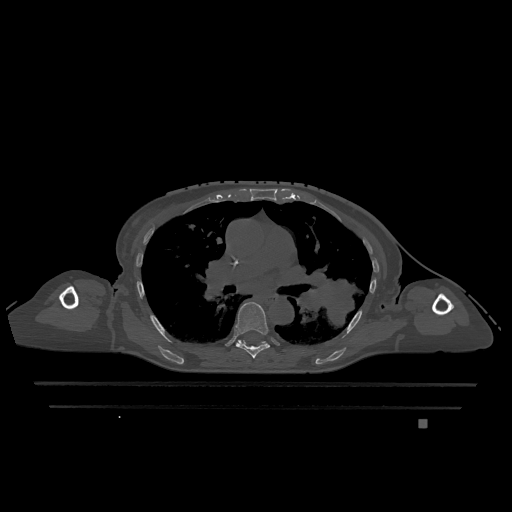
CT including the spine, one axial slice; position 780 of 1317 along the scan axis; bone window (W 1800 / L 400 HU); 512 × 512 image matrix. Patient: female, 74 years. From the clinical record (not read from this slice): primary cancer: lung; vertebrae with lytic lesions (as recorded): T1, T4, T5, T6, L4, L5.
Annotated regions visible in this slice (semi-automatically segmented with operator editing):
- T6 vertebra: box from (x=235, y=302) to (x=270, y=359) px
- T7 vertebra: (x=238, y=340)–(x=269, y=345)